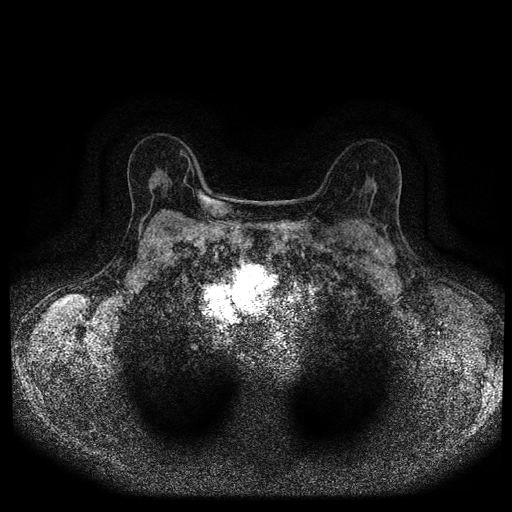
Breast MRI (dynamic contrast-enhanced, multi-phase), one axial slice; position 64 of 116 along the scan axis; dynamic contrast-enhanced series, time point 2 of 5 at this slice position (early post-contrast); 1.5 T; TE 2.7 ms, TR 5.4 ms; 2 mm slice thickness; 512 × 512 image matrix, field of view 330 × 330 mm. Female patient, age 63 years.
Structures marked on this image (semi-automatically segmented with operator editing):
- breast lesion (labelled 'tumour' in the annotation; benign lesions carry a separate 'benign' label): bounding box [x1, y1, x2, y2] px = [382, 223, 392, 232]